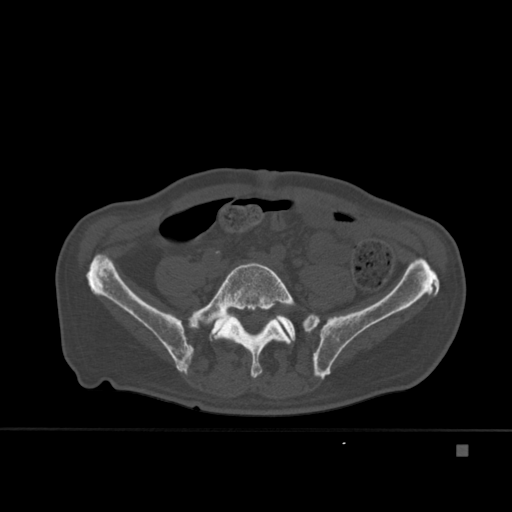
CT including the spine, one axial slice; slice 102 of 451 in the series (ordered by position); bone window (W 1800 / L 400 HU); 1.5 mm slice thickness; 512 × 512 image matrix, field of view 378 × 378 mm. Patient: male, 75 years. From the clinical record (not read from this slice): primary cancer: prostate.
Annotated regions visible in this slice (semi-automatic segmentation, software-assisted and operator-edited):
- L5 vertebra: box from (x=188, y=262) to (x=295, y=378) px
- T7 vertebra: (x=209, y=296)–(x=247, y=333)